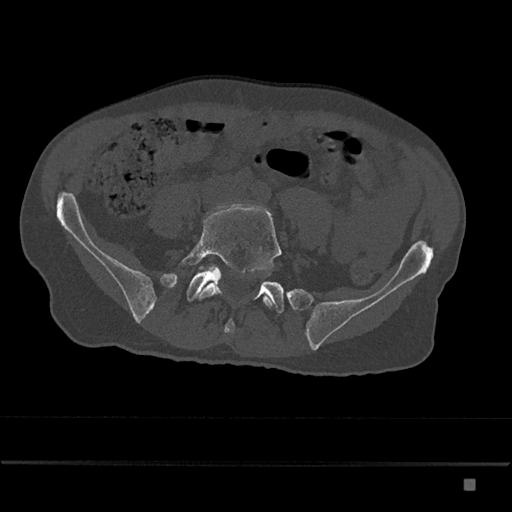
CT including the spine, one axial slice; slice 263 of 797 in the series (ordered by position); 120 kVp; bone window (W 1800 / L 400 HU); 0.5 mm slice thickness; 512 × 512 image matrix, field of view 390 × 390 mm. Patient: male, 72 years. From the clinical record (not read from this slice): primary cancer: prostate.
Annotated regions visible in this slice (semi-automatic segmentation, software-assisted and operator-edited):
- L5 vertebra: bounding box [x1, y1, x2, y2] px = [182, 207, 282, 308]